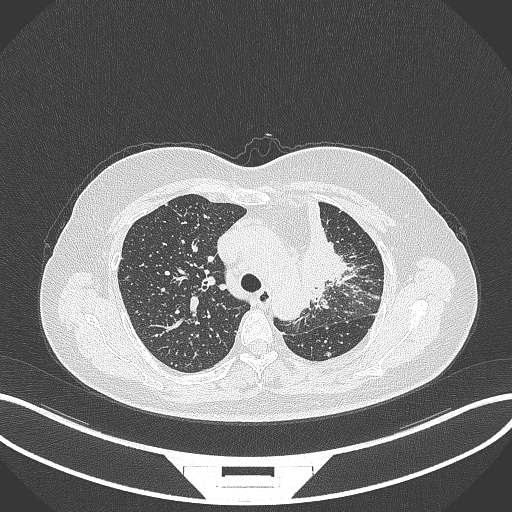
Chest CT, one axial slice. Lung window (W 1500 / L -600 HU). 1 mm slice thickness. 512 × 512 image matrix, field of view 400 × 400 mm. Female patient, age 49 years. From the clinical record (not read from this slice): clinical TNM (as recorded): T1c N0 M1.
Outlined on this slice (bounding box drawn by a radiologist):
- lung tumour (recorded histology: adenocarcinoma): bounding box <295,196,359,303> (left, top, right, bottom; pixels)